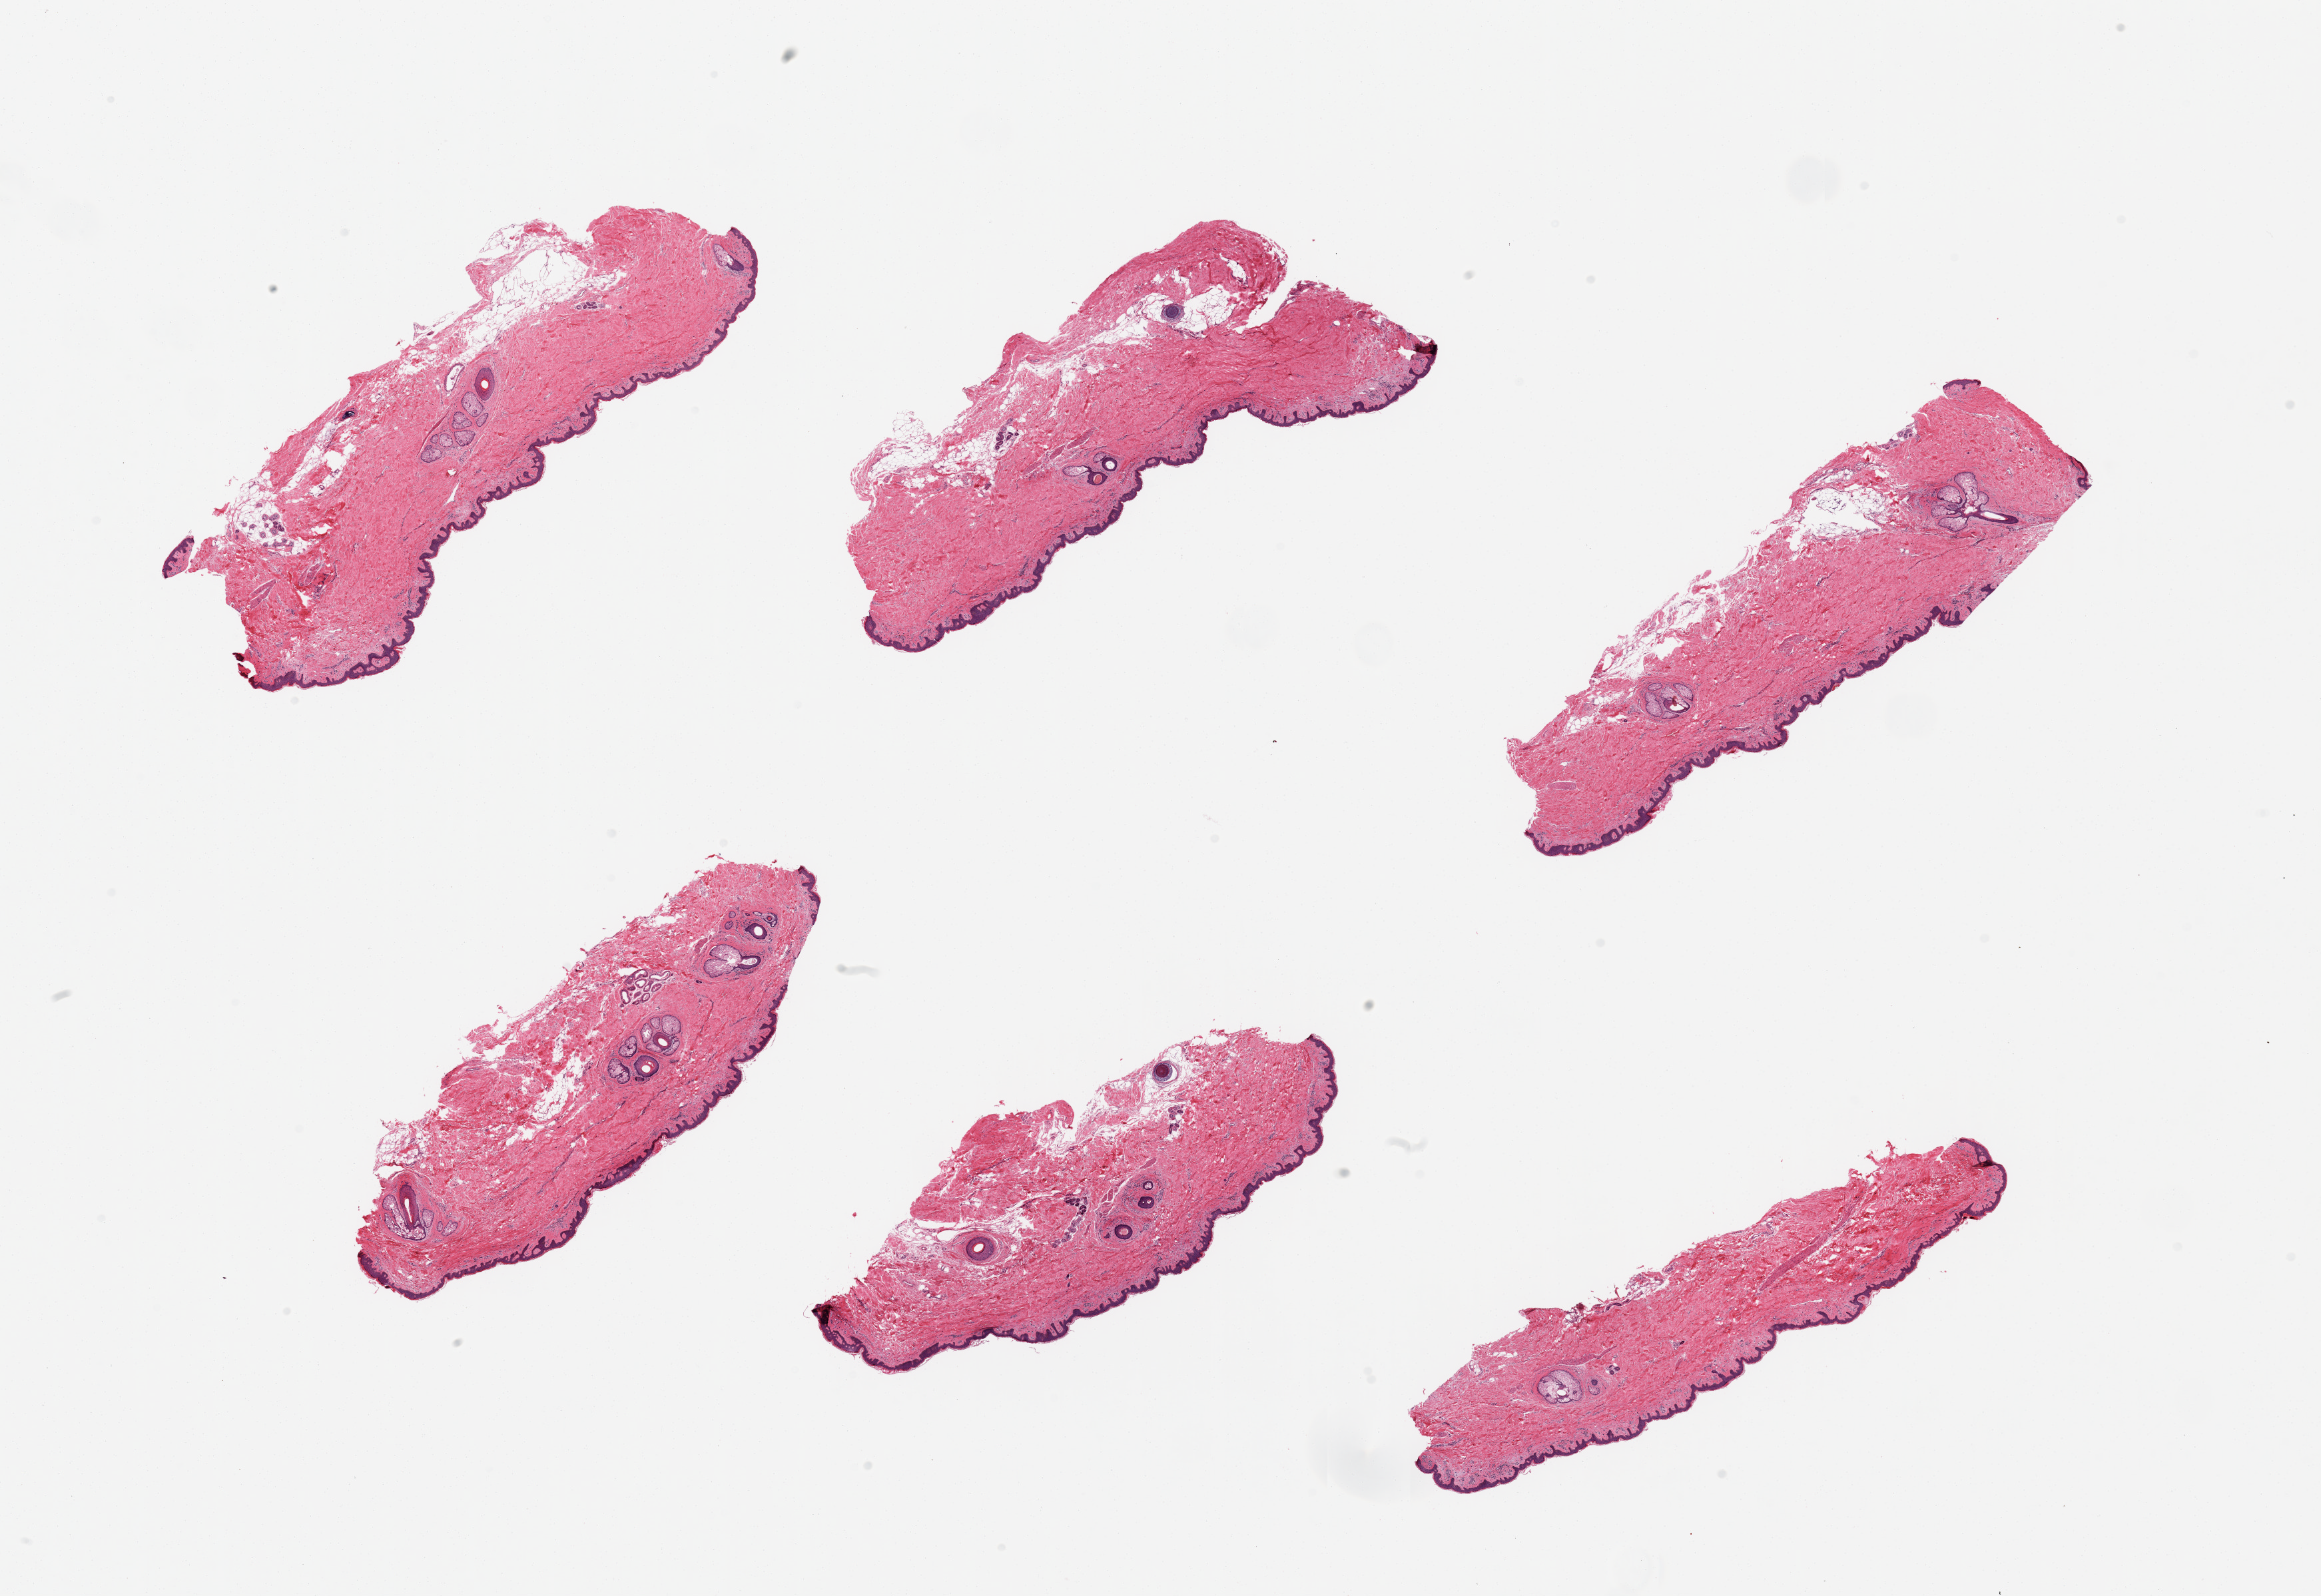
H&E whole-slide image, shown as a low-resolution overview of the whole scanned area (about 27.6 x 19.0 mm); PAXgene-fixed, paraffin-embedded tissue; target tissue: skin of suprapubic region; tissue donor sample.
Review note (as recorded): 6 pieces; well trimmed; up to 5 hair follicles per section; 10% intradermal fat.